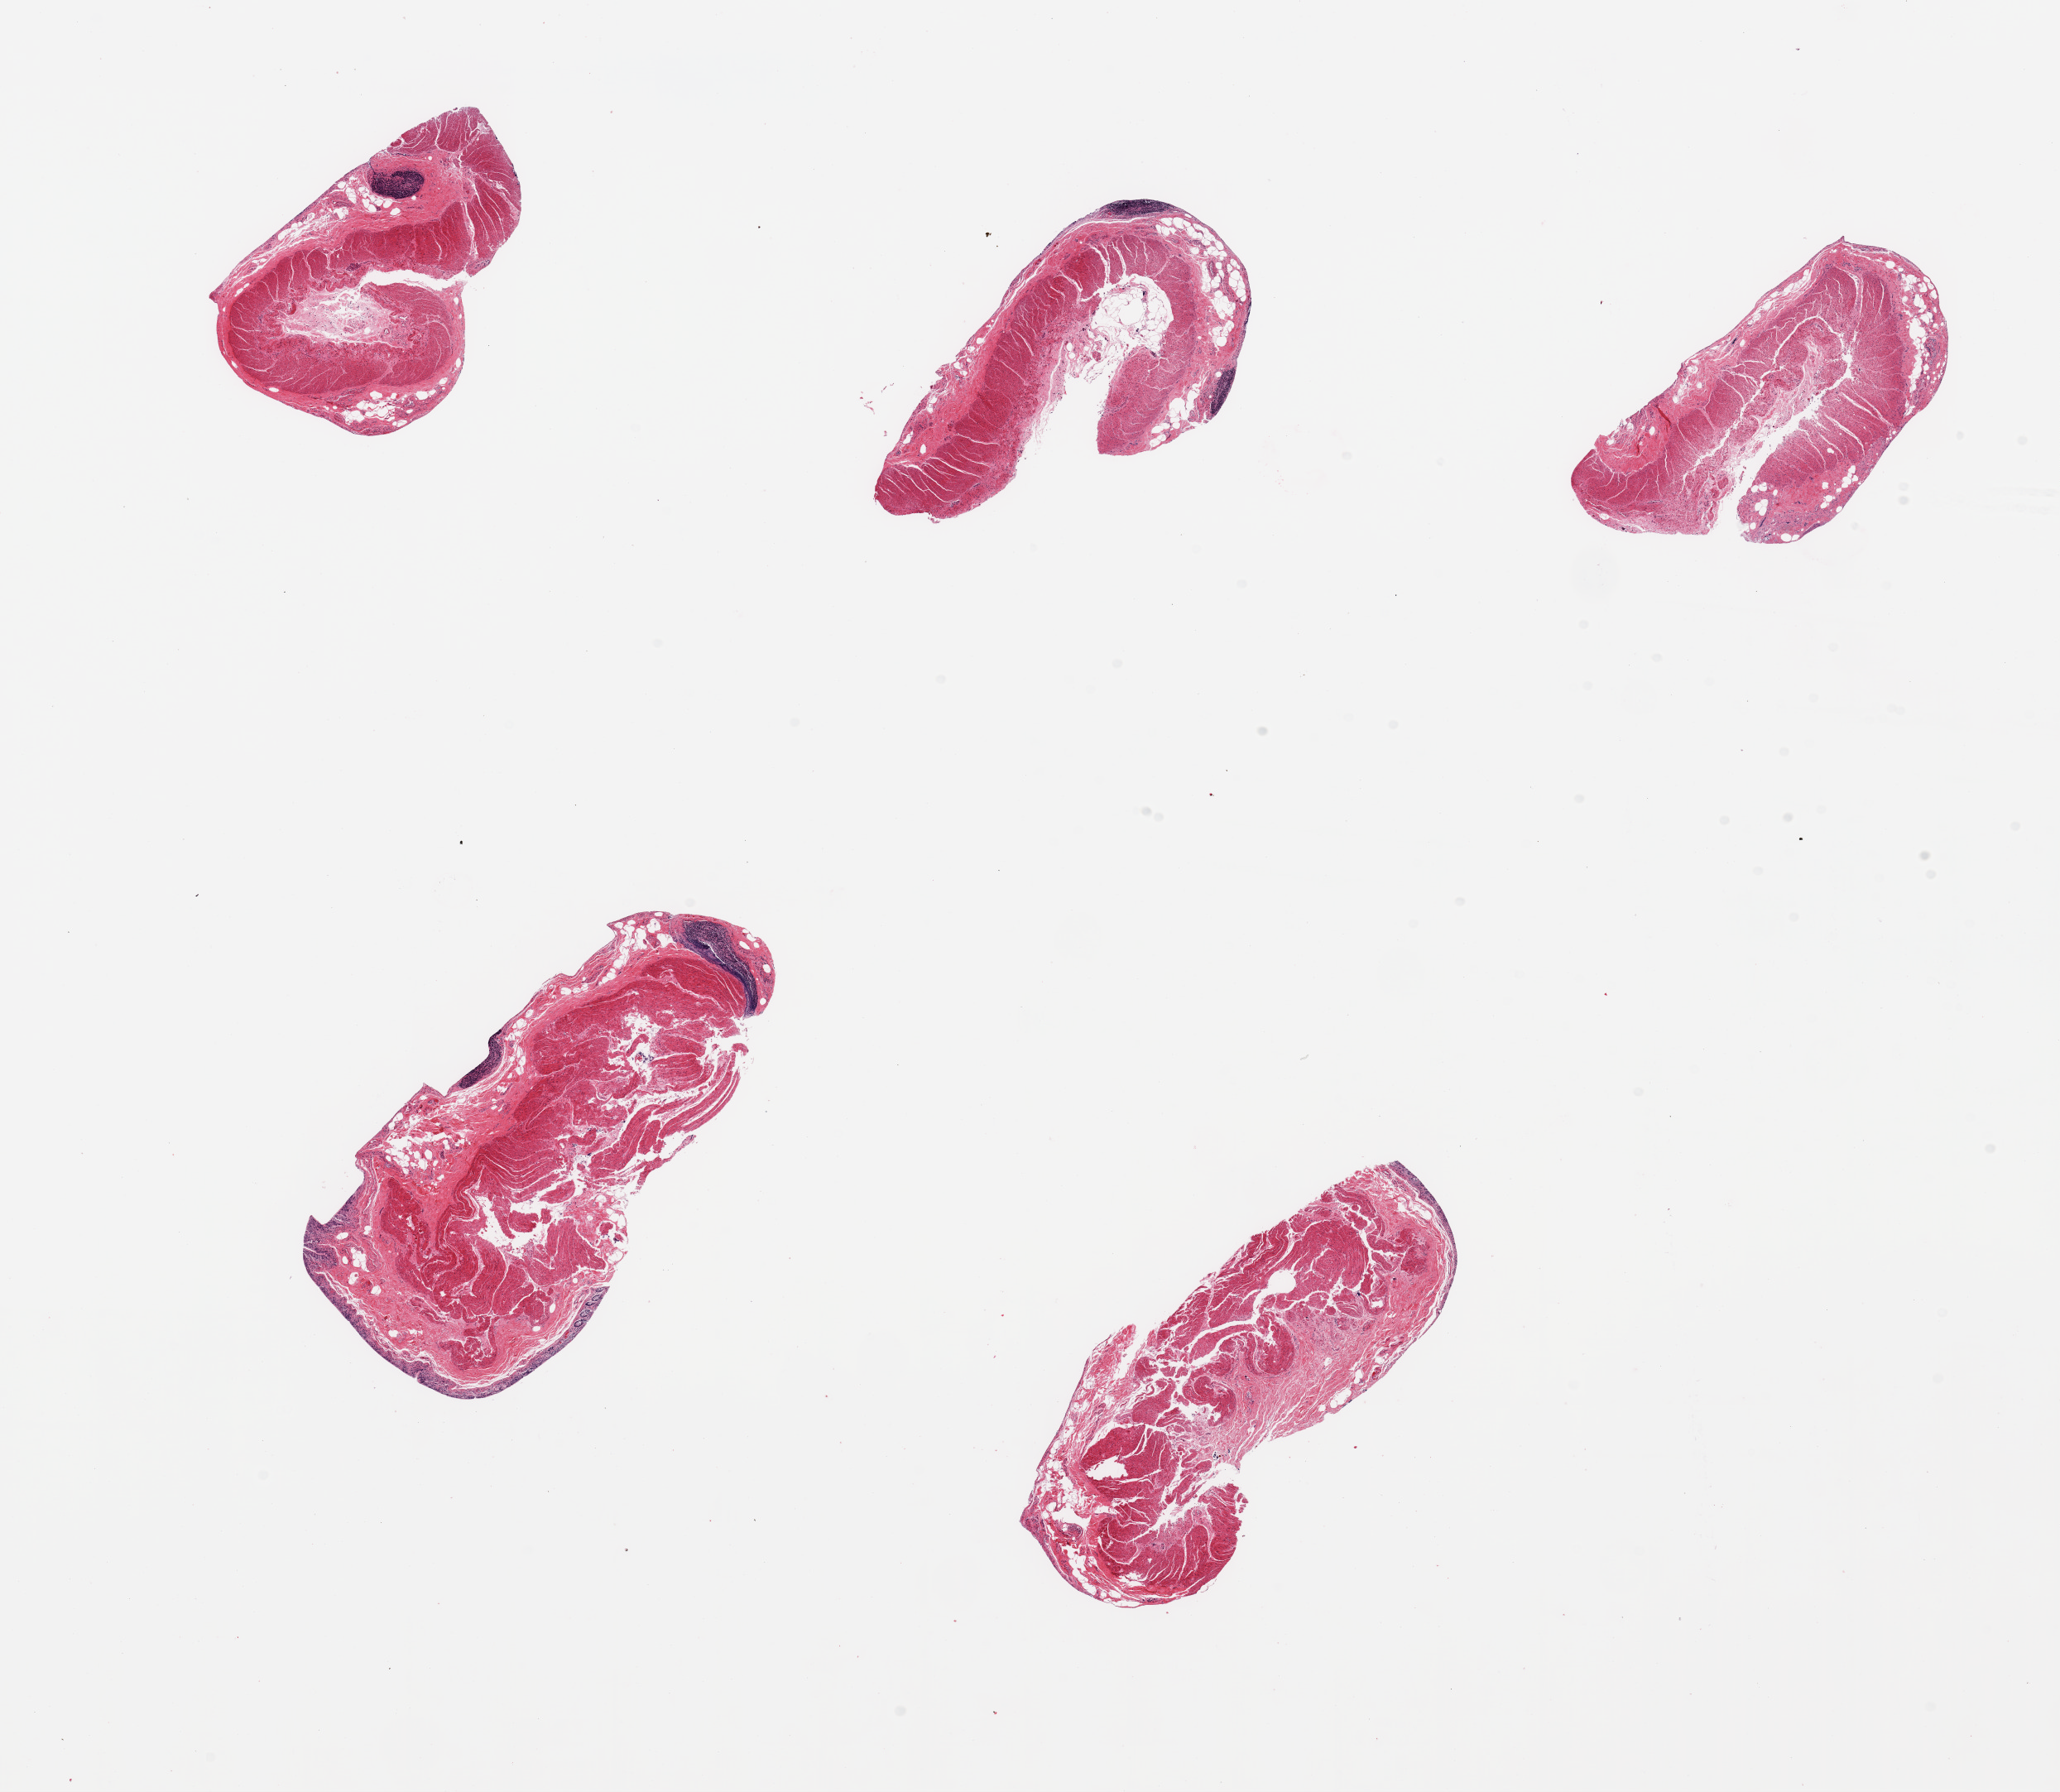
Whole-slide image, hematoxylin and eosin (H&E) stain — a low-resolution overview of the entire scanned area, about 19.7 x 17.1 mm, PAXgene-fixed, paraffin-embedded tissue, sampled site (target tissue): sigmoid colon, donor tissue sample. Donor sex: male.
Reviewer comment on this tissue sample: 5 pieces; predominantly muscularis with several strips of residual autolyzed mucosa.